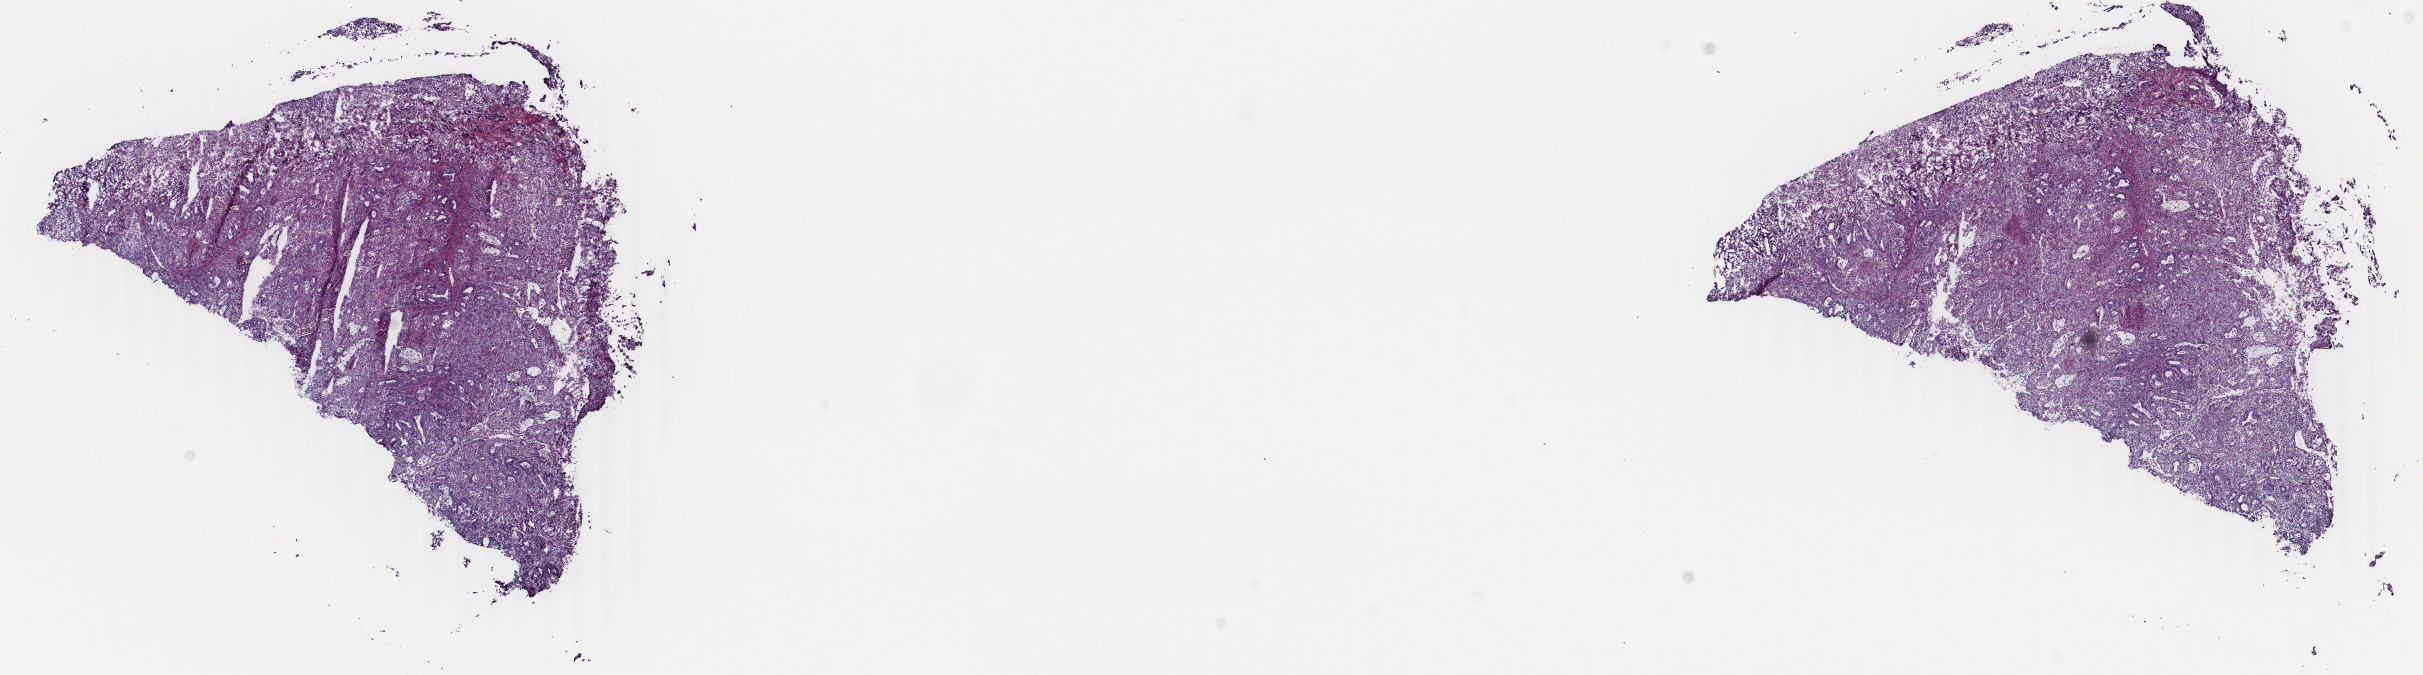
Digitized H&E tissue section (whole slide) — a low-resolution overview of the entire scanned area, about 19.3 x 5.4 mm (acquisition: 40x scan); frozen section from the top of the tissue portion; uterus, primary tumour sample. Female, age 69 years at initial diagnosis. Histologic grade: G2 (moderately differentiated). Composition of this section per pathologist review: tumour cells 70%, tumour nuclei 70%, normal cells 0%, stromal cells 20%, necrosis 10%. Infiltration values recorded for this section: lymphocyte infiltration 30%, monocyte infiltration 10%, neutrophil infiltration 50%.
Lymph nodes positive (case pathology): 0 of 42 examined. Histologic diagnosis: Endometrioid adenocarcinoma, NOS (endometrium). FIGO stage: IB.